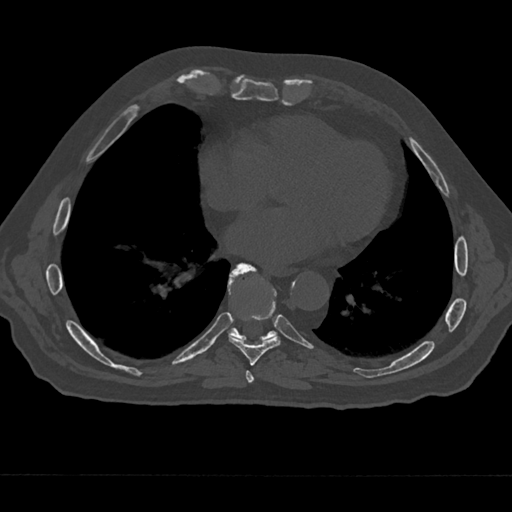
CT including the spine, one axial slice; position 298 of 797 along the scan axis; 120 kVp; bone window (W 1800 / L 400 HU); 512 × 512 image matrix, field of view 377 × 377 mm. Male patient, age 75 years. Case-level facts recorded for this patient, not image findings: primary cancer: renal.
Annotated regions visible in this slice (semi-automatically segmented with operator editing):
- T7 vertebra: bounding box [x1, y1, x2, y2] px = [243, 369, 259, 385]
- T8 vertebra: [228, 267, 281, 366]
- T9 vertebra: [228, 263, 277, 342]